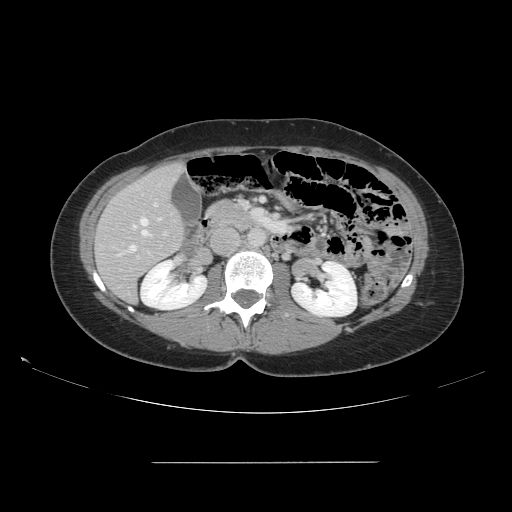
Contrast-enhanced abdominal CT, one axial slice; position 67 of 151 along the scan axis; intravenous contrast given; soft-tissue window (W 400 / L 40 HU); 2.5 mm slice thickness; 512 × 512 image matrix. Female patient, age 46 years. Case-level facts recorded for this patient, not image findings: diagnosis: colorectal cancer liver metastases, imaged before liver resection; multiple liver metastases: yes; largest metastasis: 3 cm; disease in both lobes: yes.
Structures marked on this image (outlined manually by an expert reader):
- hepatic veins: bounding box <128,217,160,252> (left, top, right, bottom; pixels)
- liver: <96,164,184,302>
- planned liver remnant (the part of the liver to remain after resection): <96,164,184,302>
- portal vein (with intrahepatic branches): <137,202,168,259>